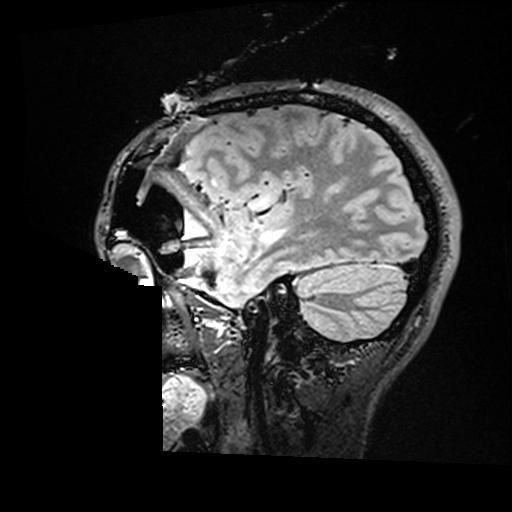
Brain MRI from a brain-tumour surgery series, one sagittal slice. Position 123 of 176 along the scan axis. T2 FLAIR. 512 × 512 image matrix, field of view 250 × 250 mm. Case-level facts recorded for this patient, not image findings: histopathology: Astrocytoma; WHO grade: 2; IDH mutation: yes; tumour location: Right Insular.
Outlined on this slice (expert manual segmentation):
- residual tumour: bounding box <260,191,273,206> (left, top, right, bottom; pixels)